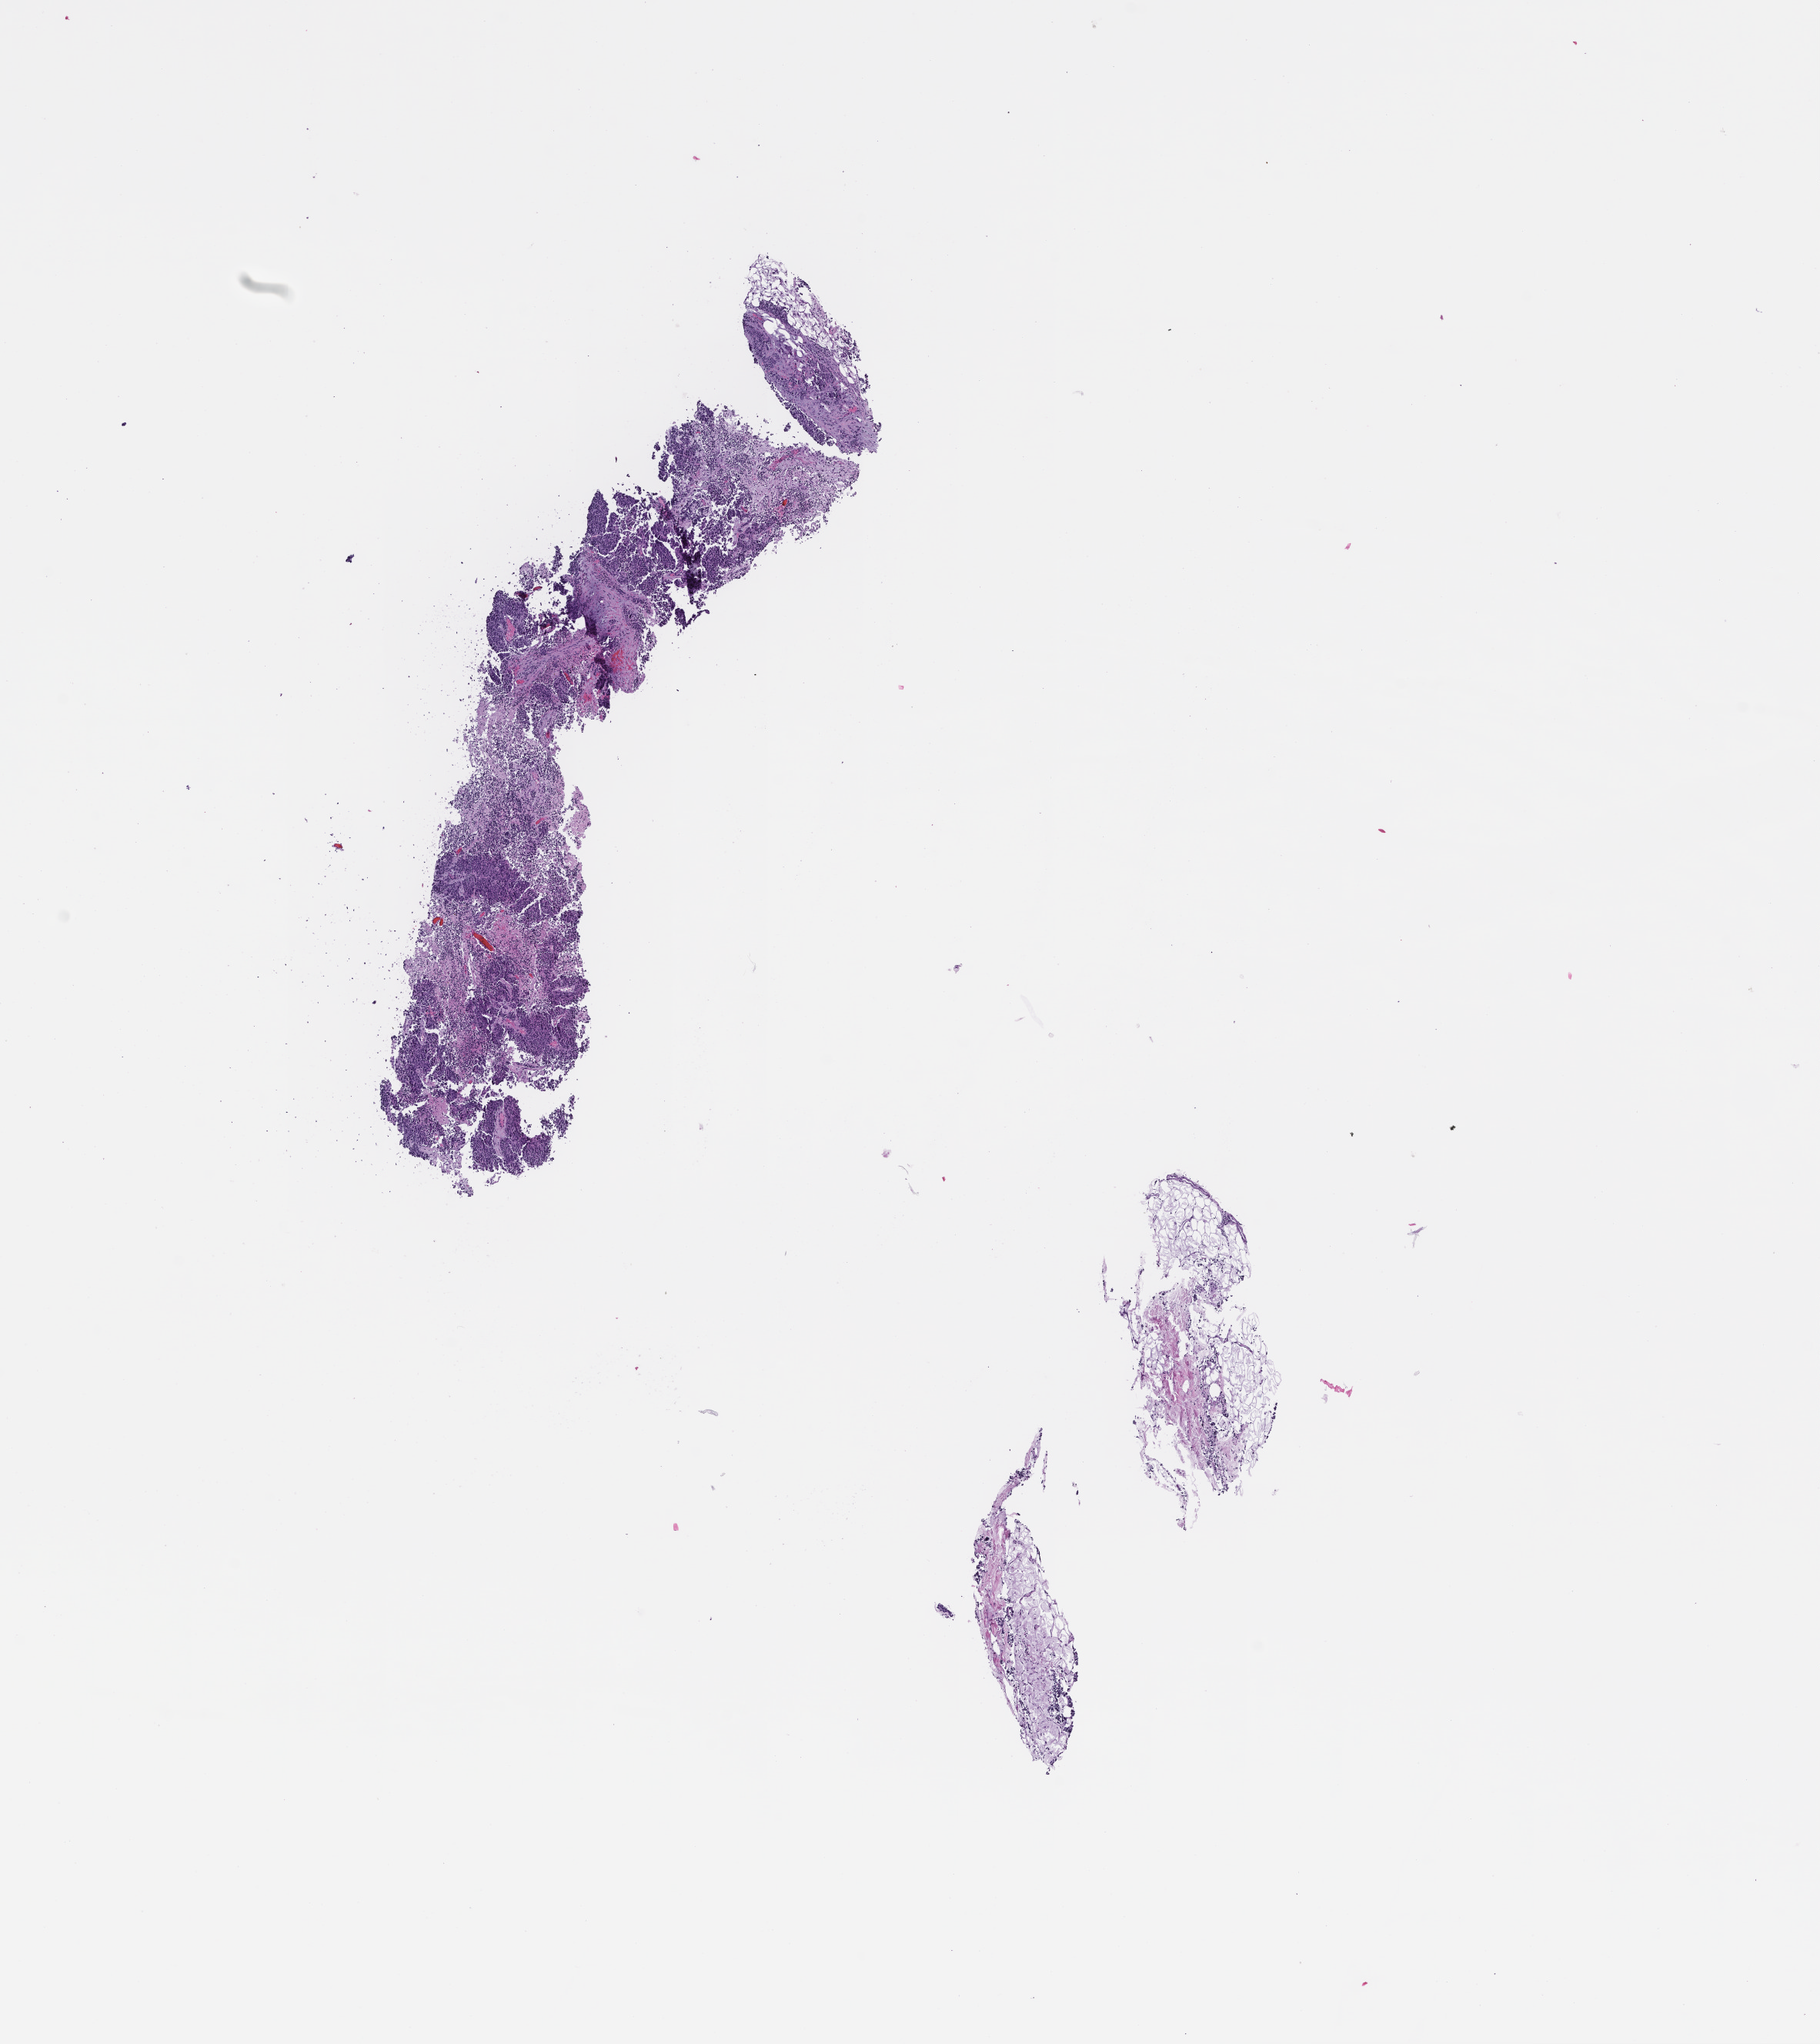
Whole-slide image, haematoxylin and eosin stain — a low-resolution overview of the entire scanned area, about 9.5 x 10.7 mm; FFPE section; specimen time point: archival tissue. Patient: female.
This section: metastasis (sampled organ not recorded). Primary diagnosis of the patient: Non-Small Cell Lung Carcinoma.